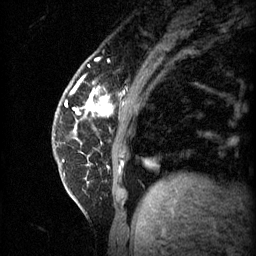
Breast MRI (dynamic contrast-enhanced), one sagittal slice. Slice 12 of 60 in the series (ordered by position). 3 images stored at this slice position (order not interpretable as contrast timing). 1.5 T. TE 4.2 ms, TR 11 ms. 256 × 256 image matrix, field of view 180 × 180 mm. Patient: female, 62 years.
Structures marked on this image (semi-automatically segmented with operator editing):
- analysis volume of interest (the breast-tissue region the enhancement analysis was run in; not a lesion): bounding box <55,72,115,135> (left, top, right, bottom; pixels)
- tumour enhancement mask (voxels above the 70 % enhancement threshold inside the analysis volume of interest): <76,88,113,115>